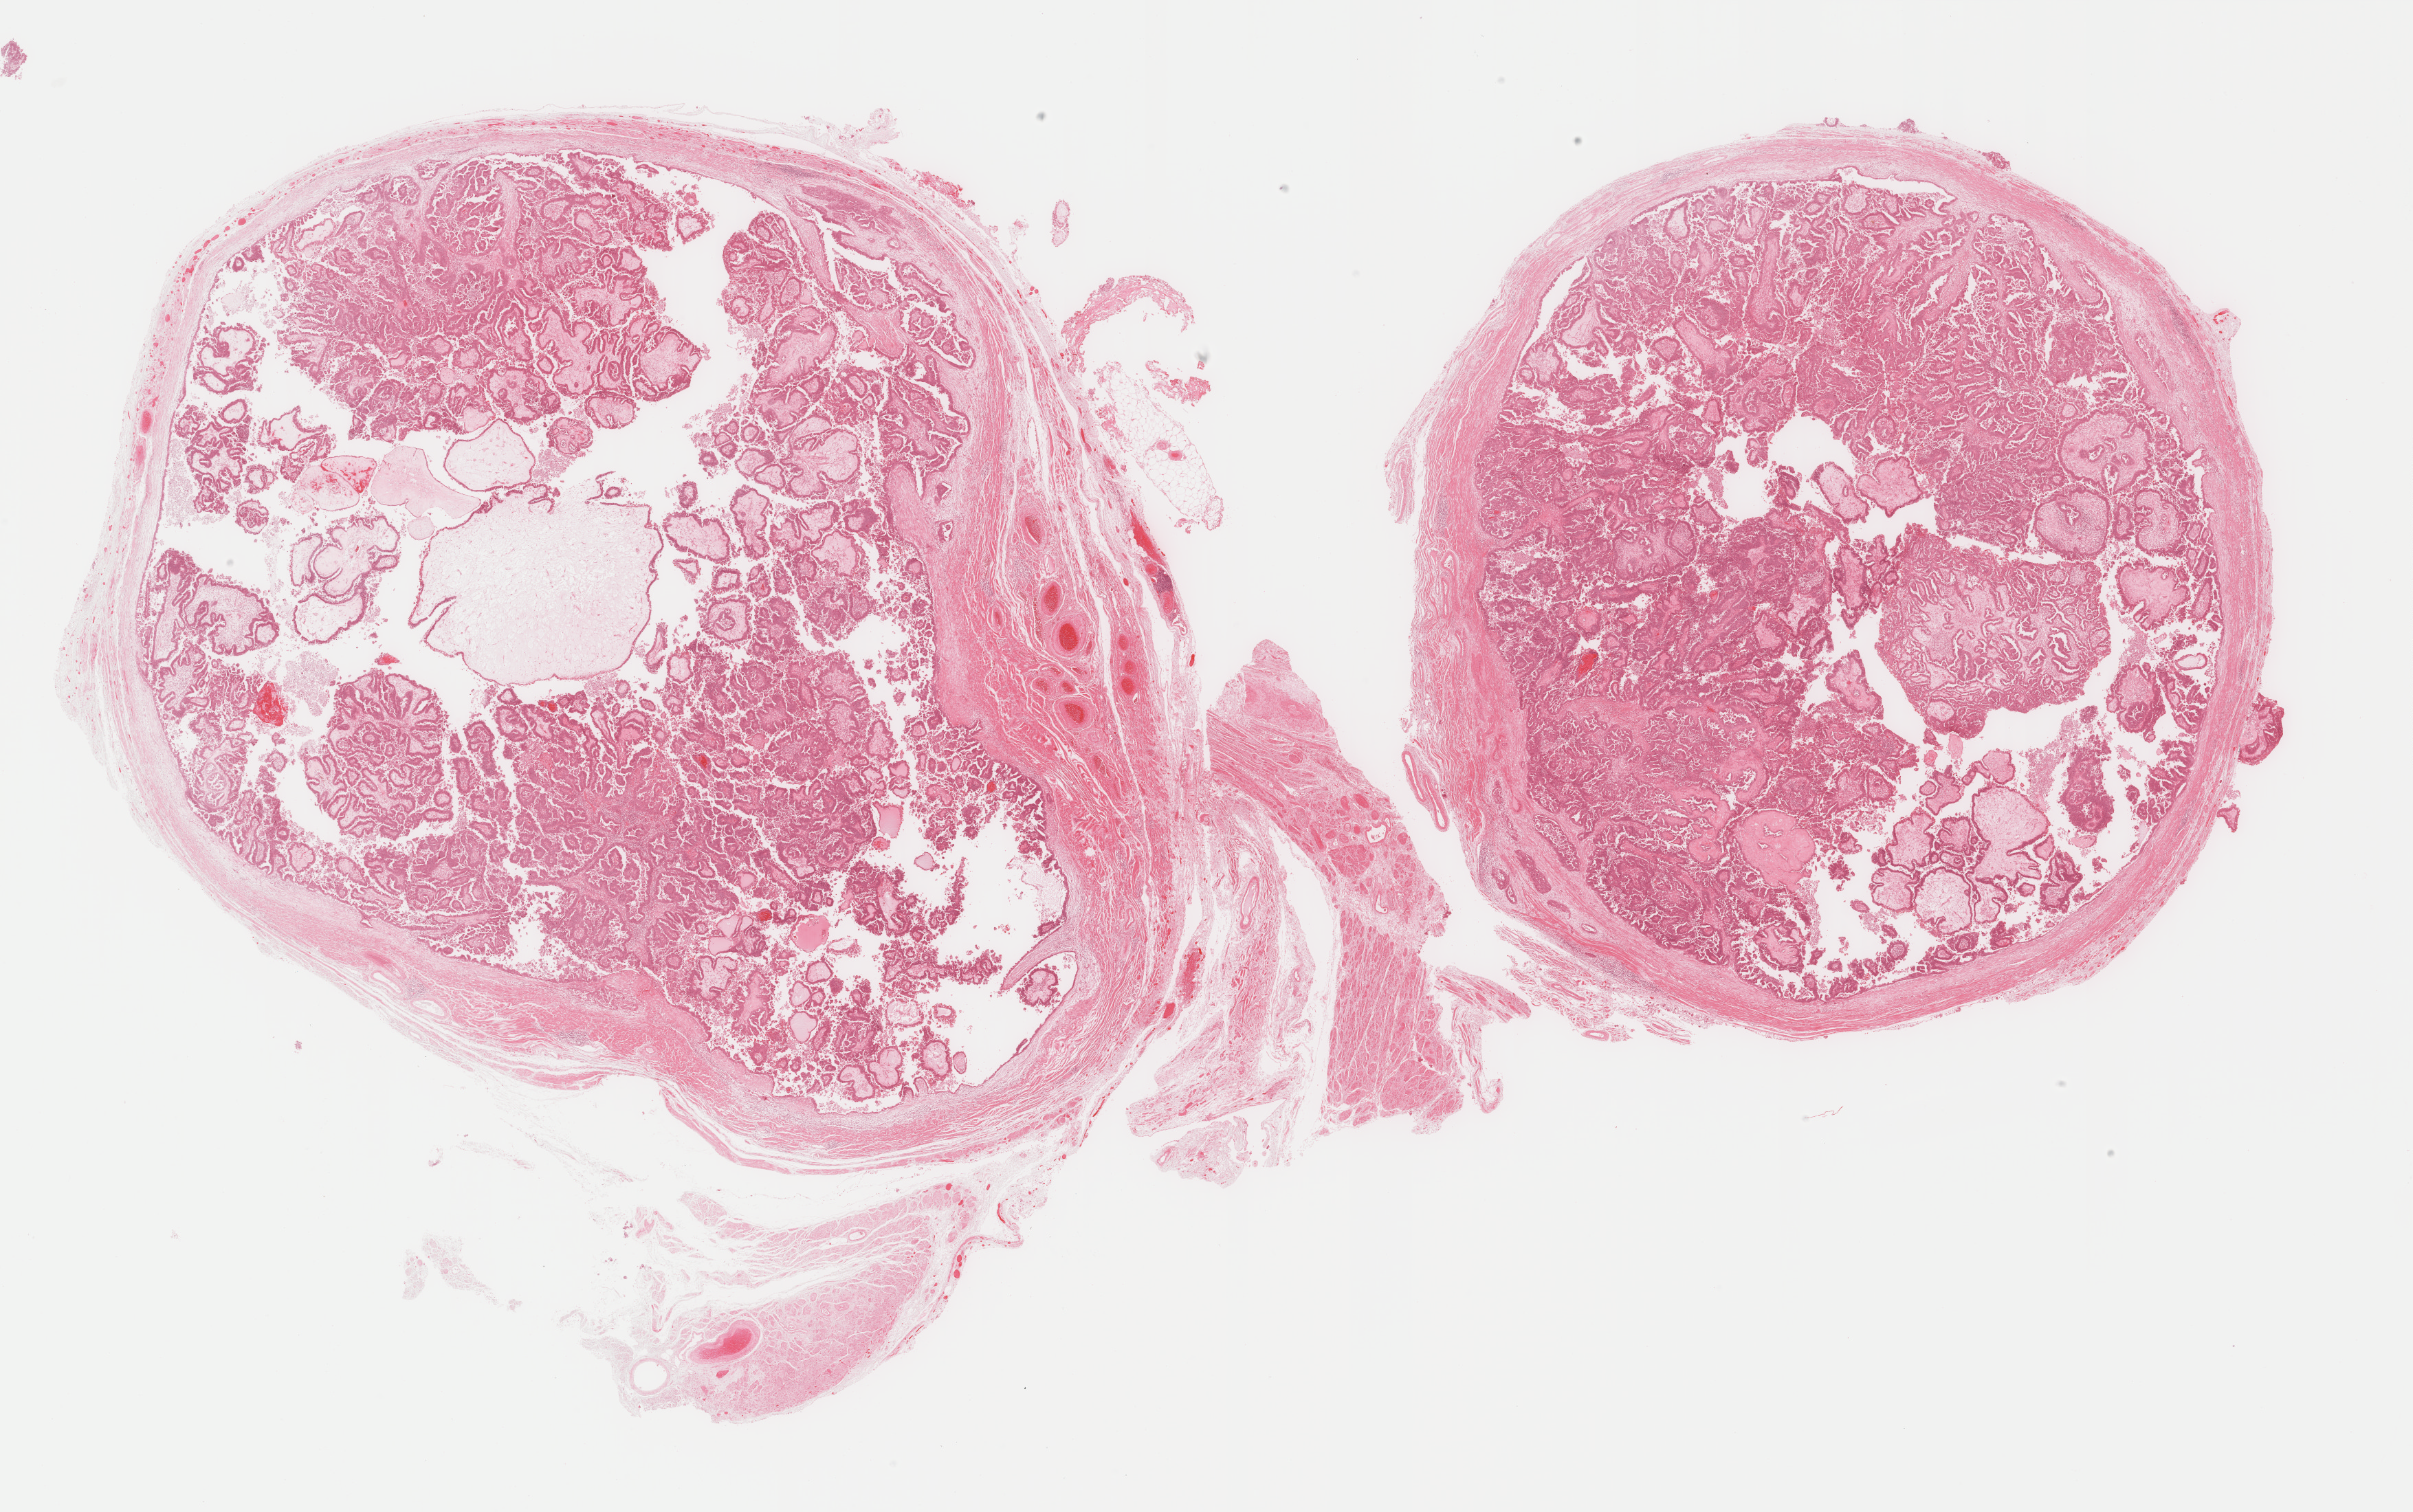
Whole-slide histology image, Hematoxylin and eosin (H&E) stained, low-resolution overview of the scanned area, about 27.9 x 17.5 mm (acquisition: 40x scan); formalin-fixed paraffin-embedded (FFPE) diagnostic section; sample: primary tumour, uterus. Female, age 67 years at initial diagnosis. Histologic grade: G3 (poorly differentiated).
• diagnosis: Serous cystadenocarcinoma, NOS (endometrium)
• FIGO stage: IIIA